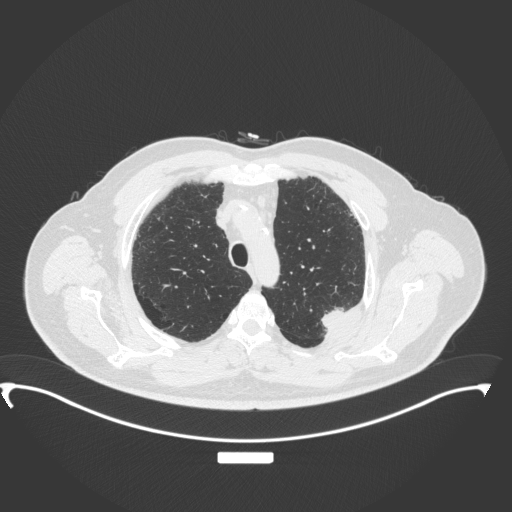
Chest CT, one axial slice; slice 284 of 350 in the series (ordered by position); reconstruction kernel B31f; lung window (W 1500 / L -600 HU); 512 × 512 image matrix. Male patient, age 64 years. From the clinical record (not read from this slice): clinical TNM (as recorded): T1c N1 M1.
Structures marked on this image (bounding box drawn by a radiologist):
- lung tumour (recorded histology: adenocarcinoma): bounding box (x1, y1, x2, y2) in pixels: (316, 300, 345, 328)